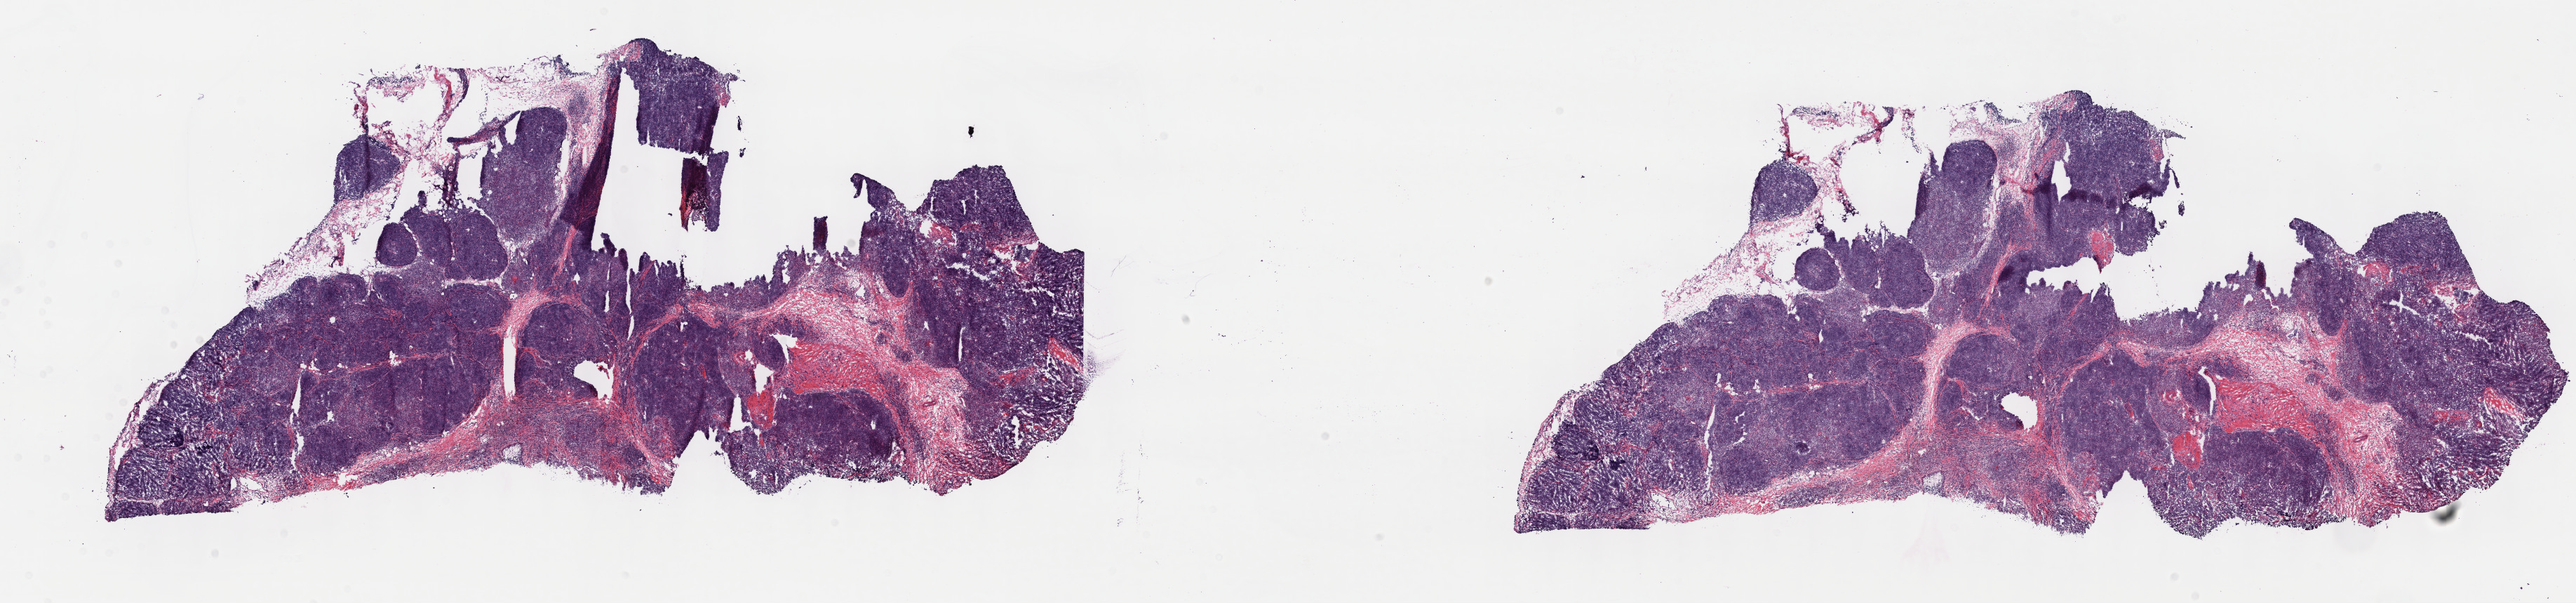
Digitized H&E tissue section (whole slide) — shown as a low-resolution overview of the whole scanned area (about 29.7 x 6.9 mm, acquisition: 40x scan). Frozen section from the top of the tissue portion. Primary tumour sample from the thymus. Male, age 44 years at initial diagnosis. Composition of this section per pathologist review: tumour cells 100%, tumour nuclei 75%, normal cells 0%, stromal cells 0%, necrosis 0%. Infiltration values recorded for this section: lymphocyte infiltration 2%, monocyte infiltration 0%, neutrophil infiltration 0%.
* histologic diagnosis: Thymoma, type B2, malignant